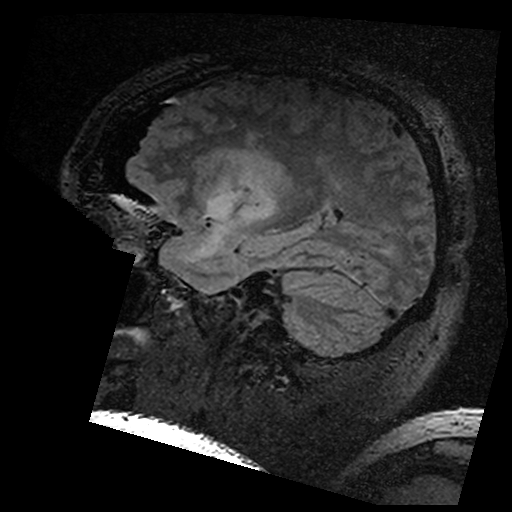
Brain MRI from a brain-tumour surgery series, one sagittal slice. Position 118 of 176 along the scan axis. T2 FLAIR. 1 mm slice thickness. 512 × 512 image matrix, field of view 250 × 250 mm. Case-level facts recorded for this patient, not image findings: histopathology: Astrocytoma; WHO grade: 3; IDH mutation: yes; tumour location: Left Insular.
Outlined on this slice (expert manual segmentation):
- residual tumour: bounding box [x1, y1, x2, y2] px = [198, 146, 288, 199]